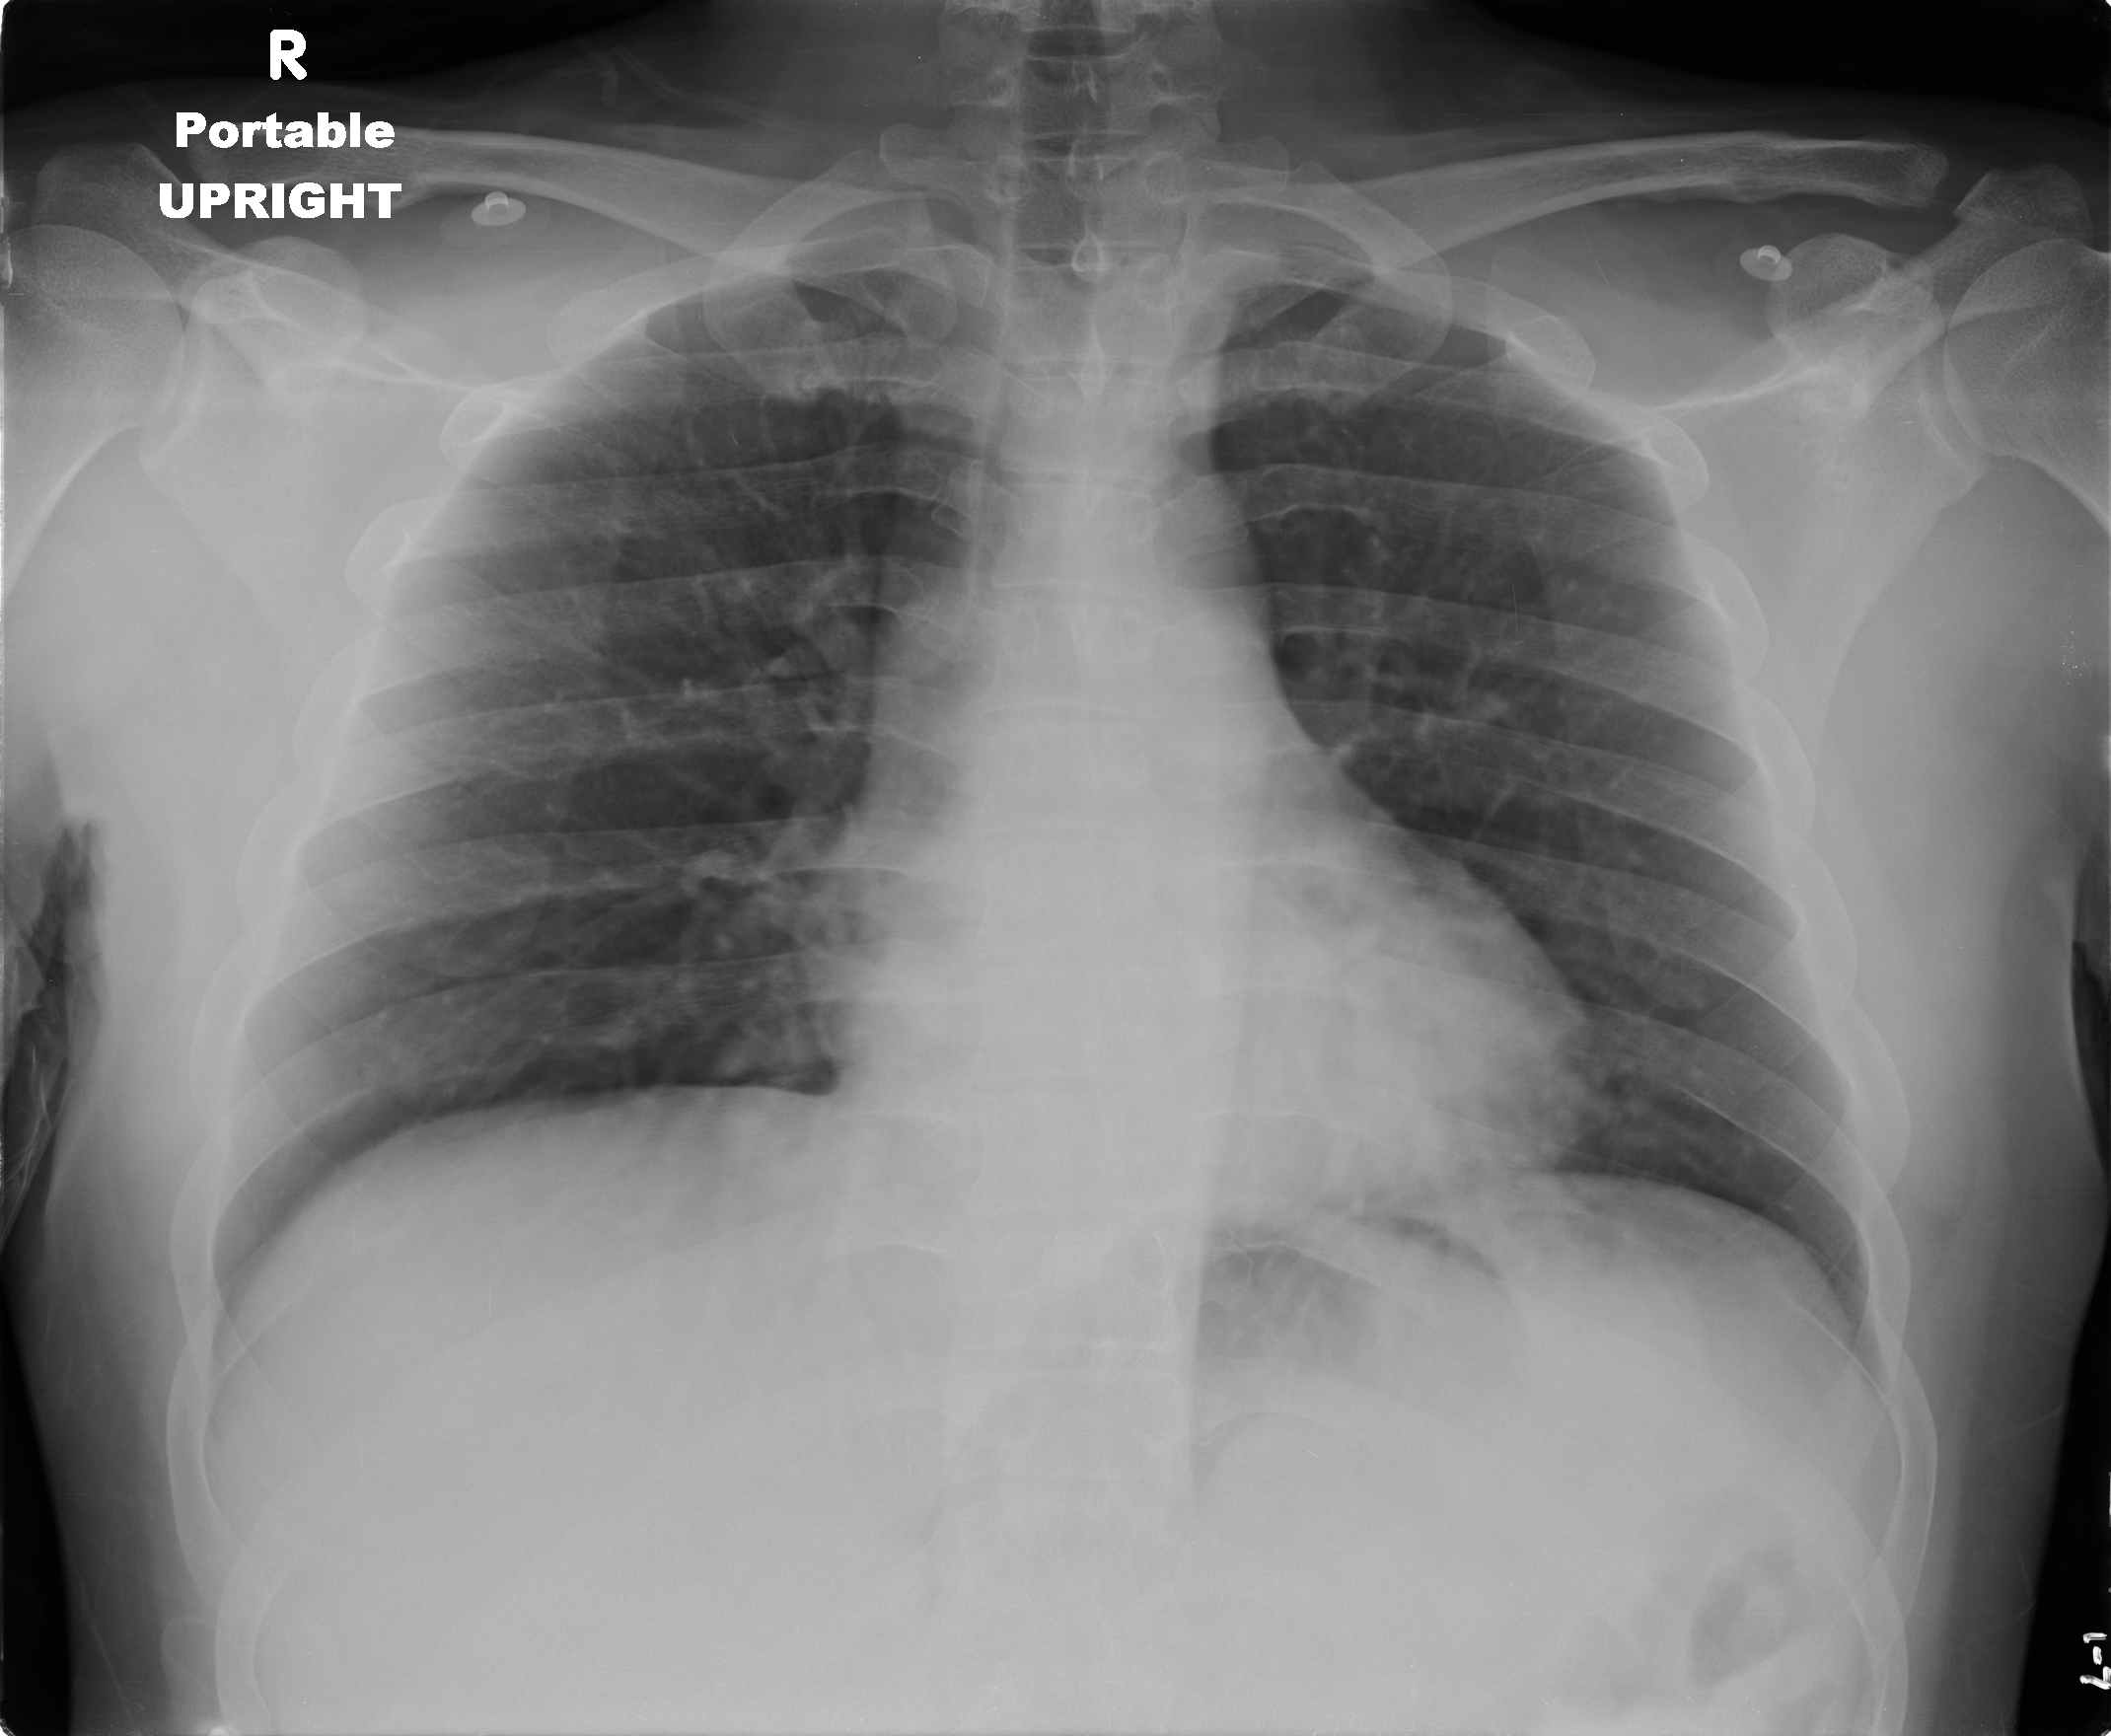
Portable chest radiograph, AP projection. Male patient, age 26 years; imaged 5 days after the COVID-19 diagnosis.
Key findings recorded by the radiologist: The lungs are clear and without focal consolidation.